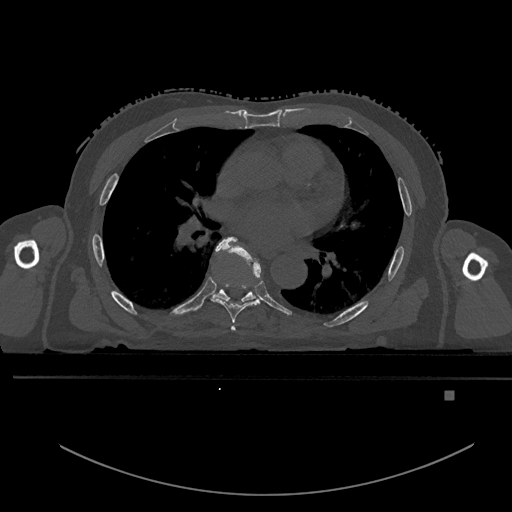
CT including the spine, one axial slice. Slice 285 of 969 in the series (ordered by position). Bone window (W 1800 / L 400 HU). 0.5 mm slice thickness. 512 × 512 image matrix. Patient: male, 82 years. Case-level facts recorded for this patient, not image findings: primary cancer: prostate; vertebrae with lytic lesions (as recorded): T11, T9, T8, T2.
Structures marked on this image (semi-automatic segmentation, software-assisted and operator-edited):
- T5 vertebra: bounding box [x1, y1, x2, y2] px = [231, 326, 236, 331]
- T6 vertebra: [211, 237, 261, 323]
- T7 vertebra: [214, 285, 256, 302]